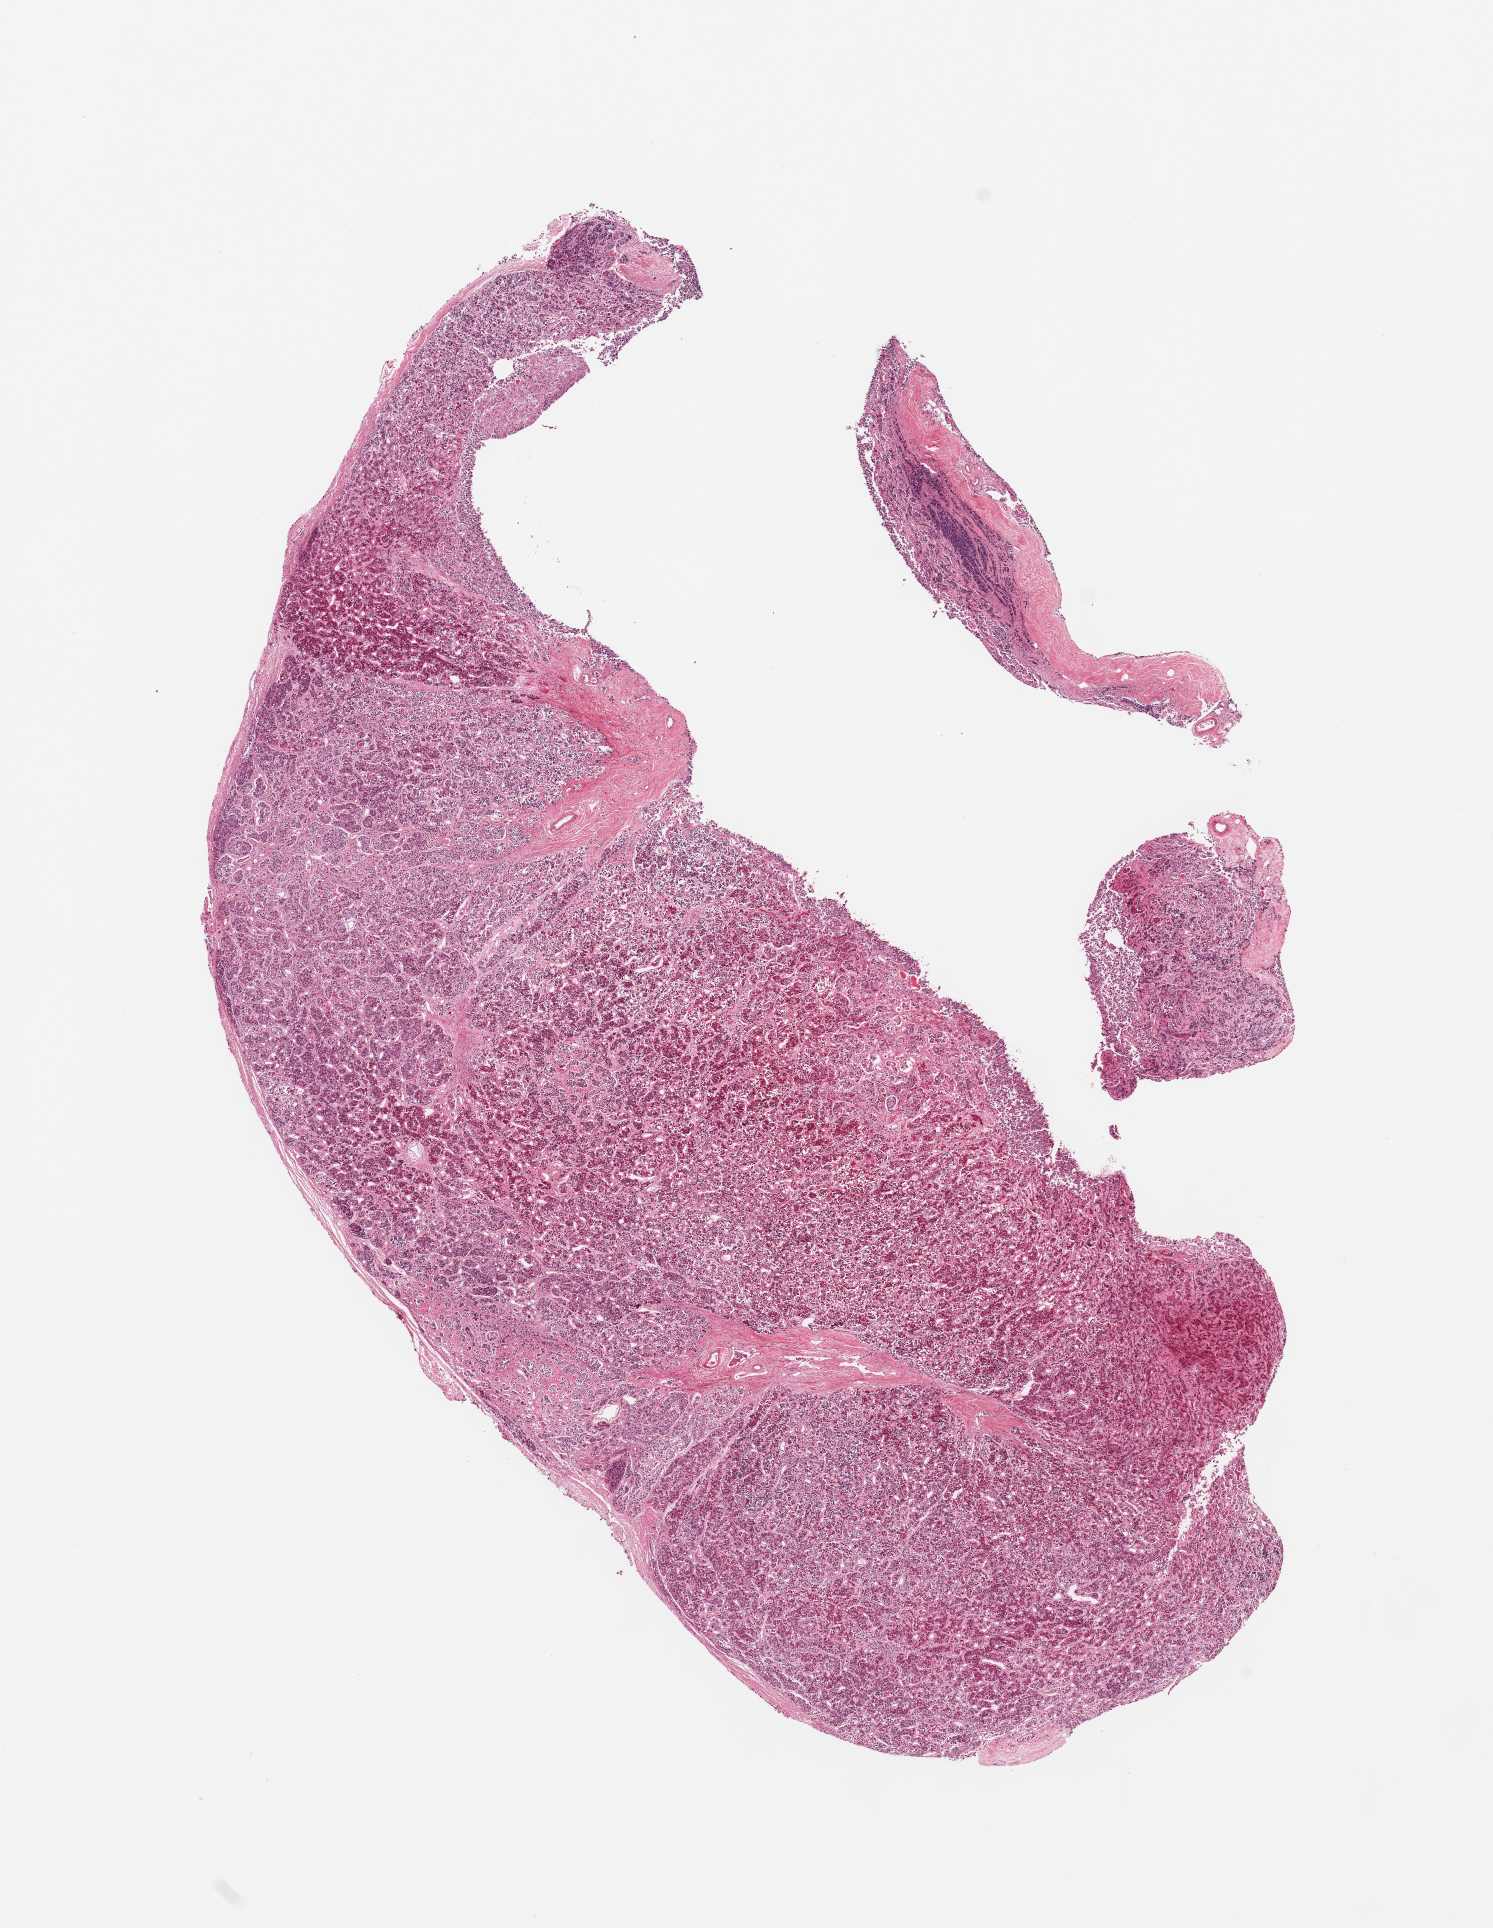
Digitized hematoxylin and eosin (H&E)-stained section, brightfield, a low-resolution overview of the entire scanned area, about 11.8 x 15.3 mm (from a 20x scan). PAXgene-fixed paraffin-embedded (PFPE) section. Section of pituitary (target tissue). Tissue donor sample. Donor sex: female.
Review note (as recorded): 1 piece; anterior.